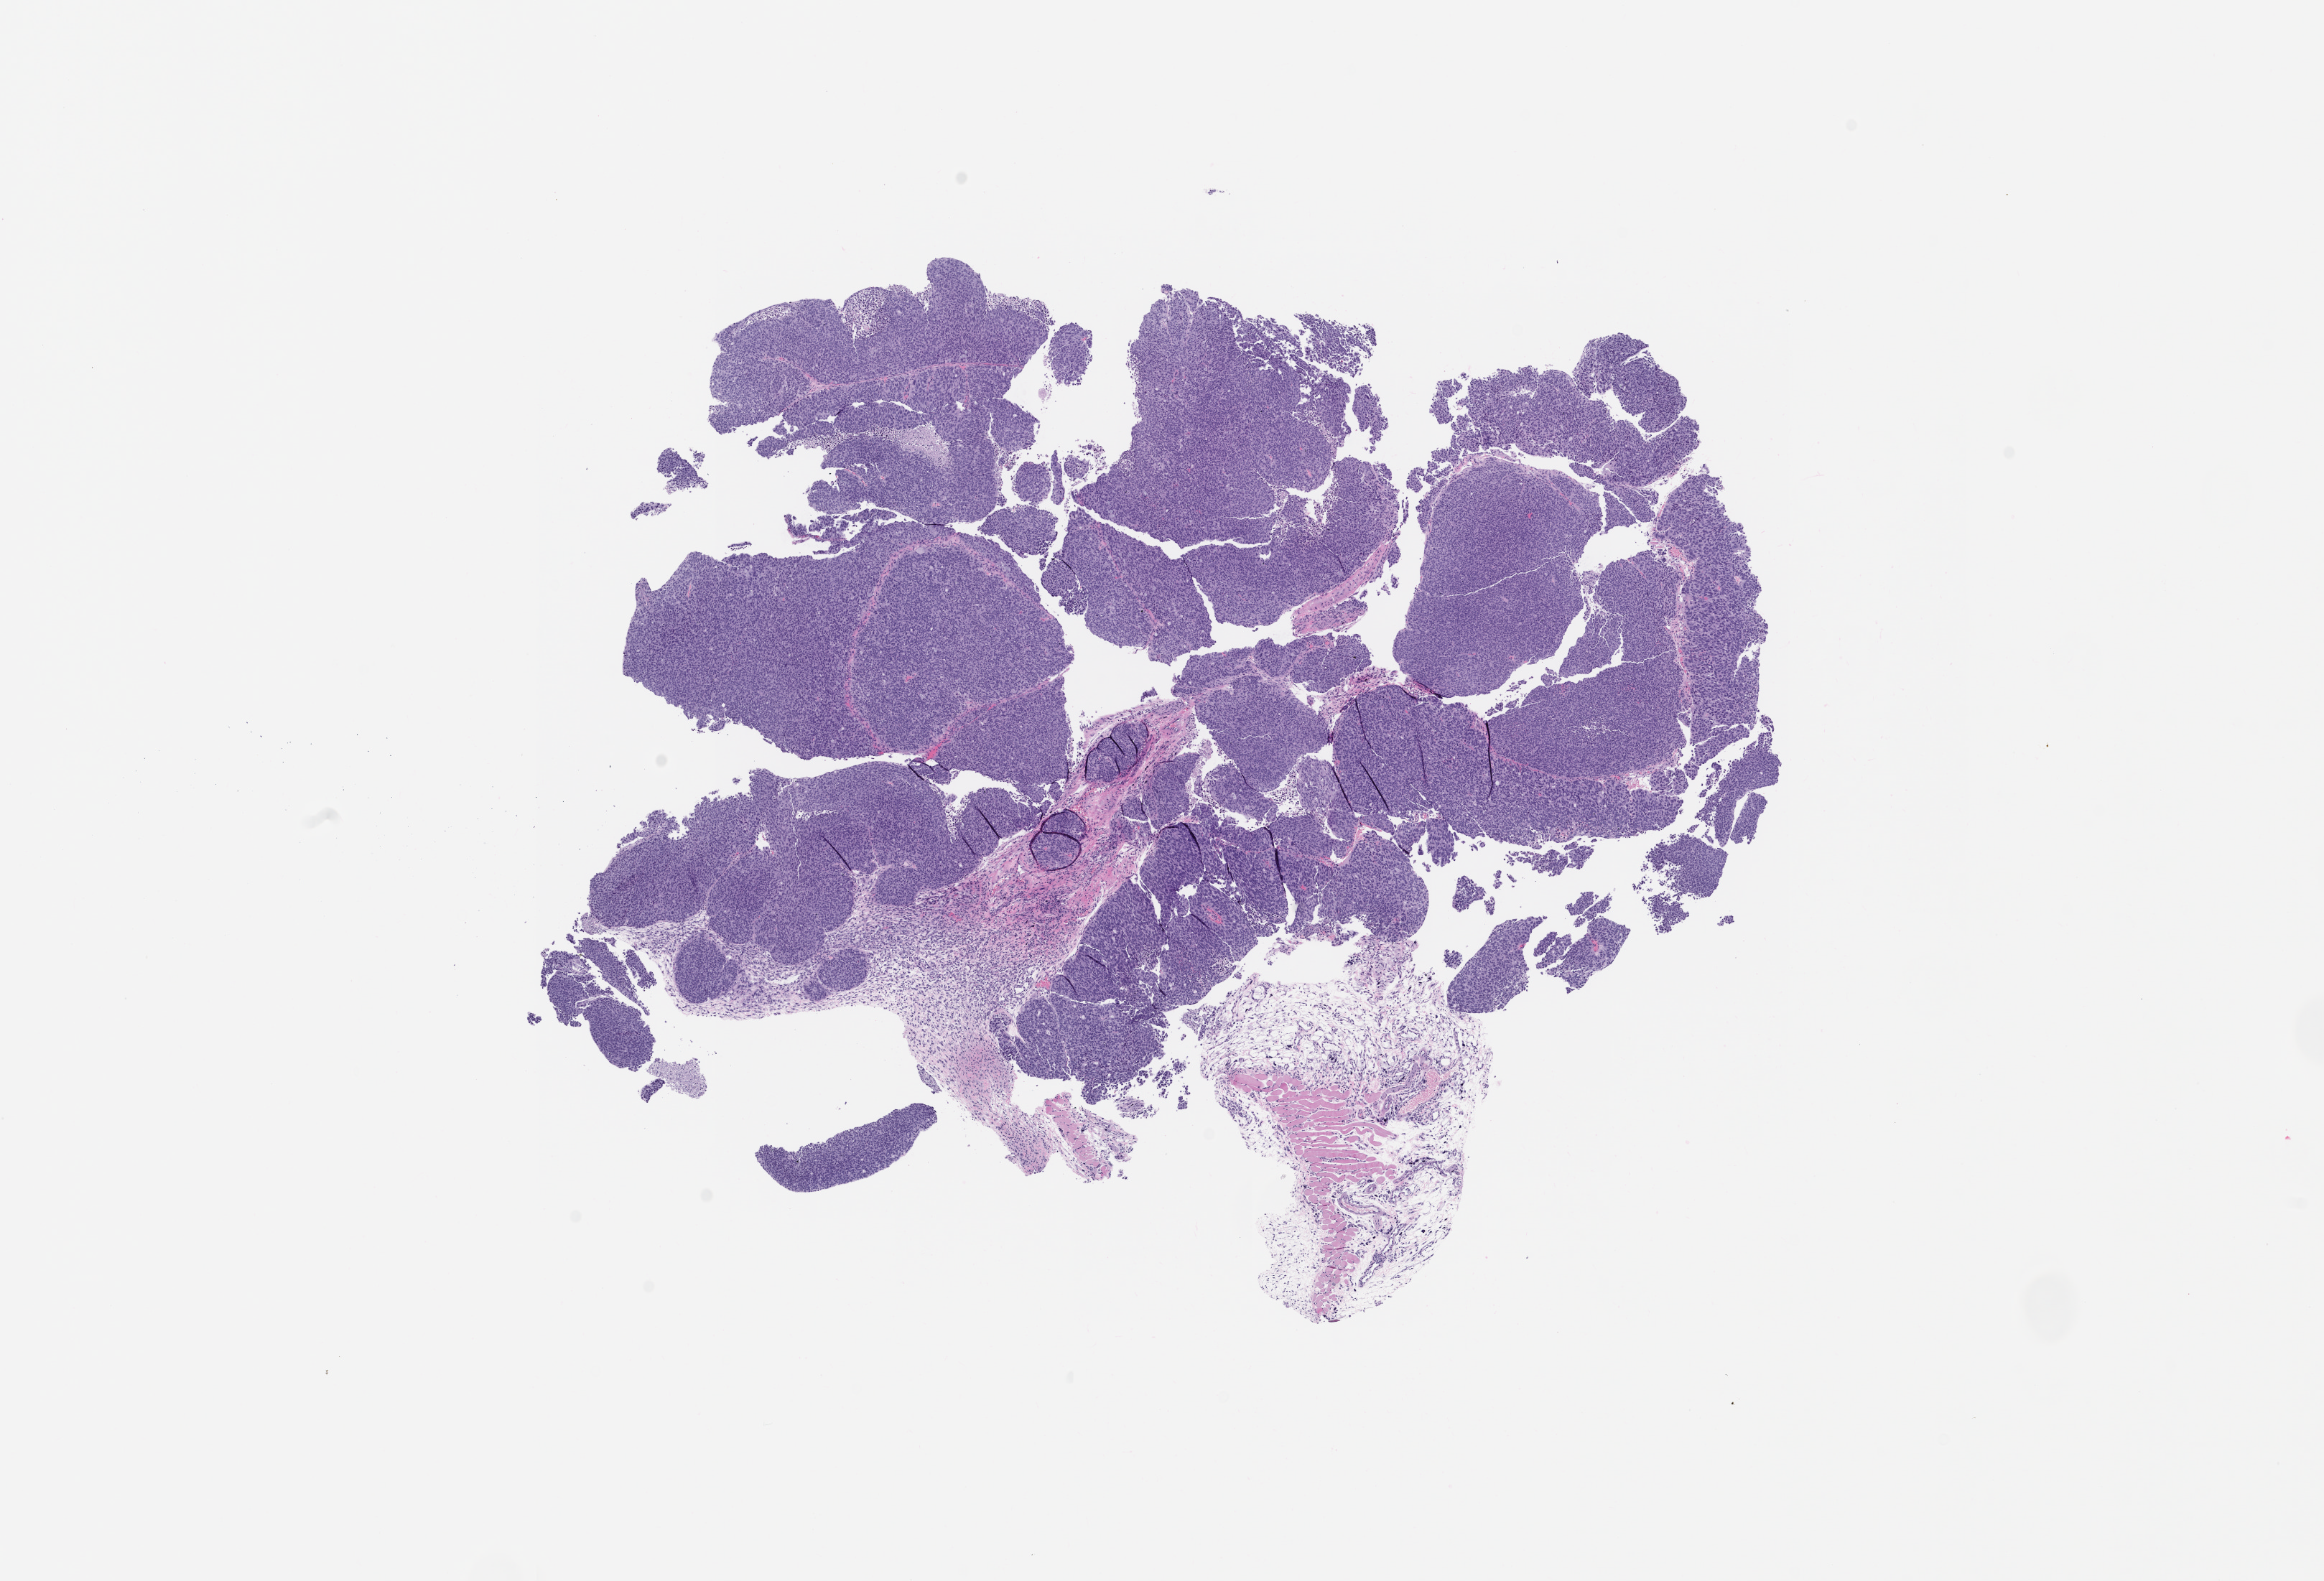
Whole-slide image, hematoxylin and eosin (H&E): patient-derived xenograft (human tumor grown in a mouse), passage 3 — whole scanned area (about 13.0 x 8.8 mm) shown as a low-resolution overview; formalin-fixed paraffin-embedded section; originating tumor site category: gastrointestinal tract.
Originating patient diagnosis: Gastric Adenocarcinoma.